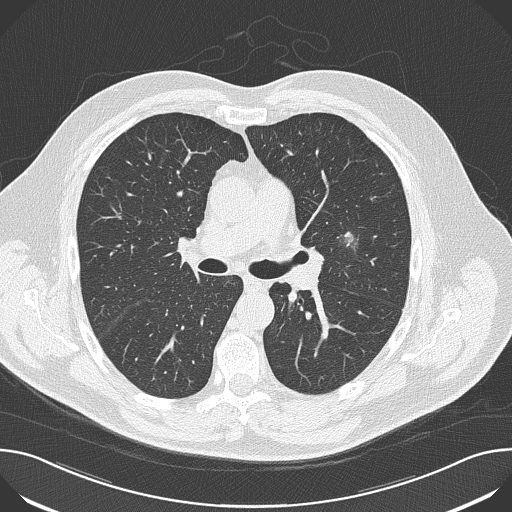
Chest CT (low-dose screening protocol), one axial image; first (baseline) screen; lung window (W 1500 / L -600 HU); 2 mm slice thickness; lung (sharp) reconstruction kernel (B50f); 512 × 512 image matrix, field of view 380 × 380 mm. Male participant, aged 65 years at enrolment. Former smoker at enrolment.
Expert reader's lesion annotation, box from (x=321, y=223) to (x=379, y=272) px. The screening reader recorded 5 non-calcified nodules or masses ≥4 mm on this exam (left upper lobe, left upper lobe, left upper lobe, right upper lobe, right middle lobe); which of them this box marks is not recorded. Official screen result: positive, change unspecified: nodule(s) >= 4 mm or enlarging nodule(s), mass(es), or other non-specific abnormalities suspicious for lung cancer. Later outcome: lung cancer diagnosed 52 days after this screen — adenocarcinoma, NOS, left upper lobe, moderately differentiated (G2), stage IA (AJCC 6th edition), 10 mm at pathology.